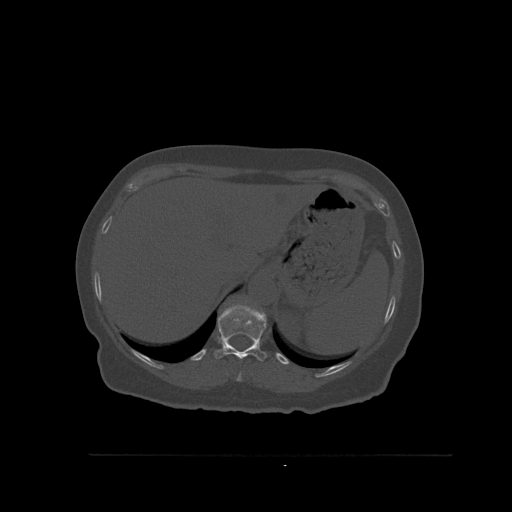
CT including the spine, one axial slice. Position 303 of 527 along the scan axis. Bone window (W 1800 / L 400 HU). 1.5 mm slice thickness. 512 × 512 image matrix, field of view 470 × 470 mm. Patient: female, 73 years. Case-level facts recorded for this patient, not image findings: primary cancer: breast.
Outlined on this slice (semi-automatically segmented with operator editing):
- T10 vertebra: box from (x=236, y=372) to (x=242, y=382) px
- T11 vertebra: (x=214, y=306)–(x=267, y=362)